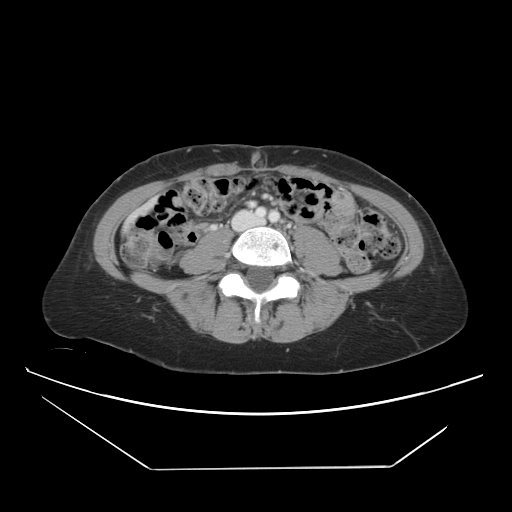
Contrast-enhanced abdominal CT, one axial slice; slice 5 of 42 in the series (ordered by position); 120 kVp; intravenous contrast given; soft-tissue window (W 400 / L 40 HU); 512 × 512 image matrix. Female patient, age 52 years. From the clinical record (not read from this slice): diagnosis: colorectal cancer liver metastases, imaged before liver resection; multiple liver metastases: yes; largest metastasis: 5.5 cm; disease in both lobes: yes.
Structures marked on this image (outlined manually by an expert reader):
- portal vein (with intrahepatic branches): bounding box [x1, y1, x2, y2] px = [250, 202, 254, 204]